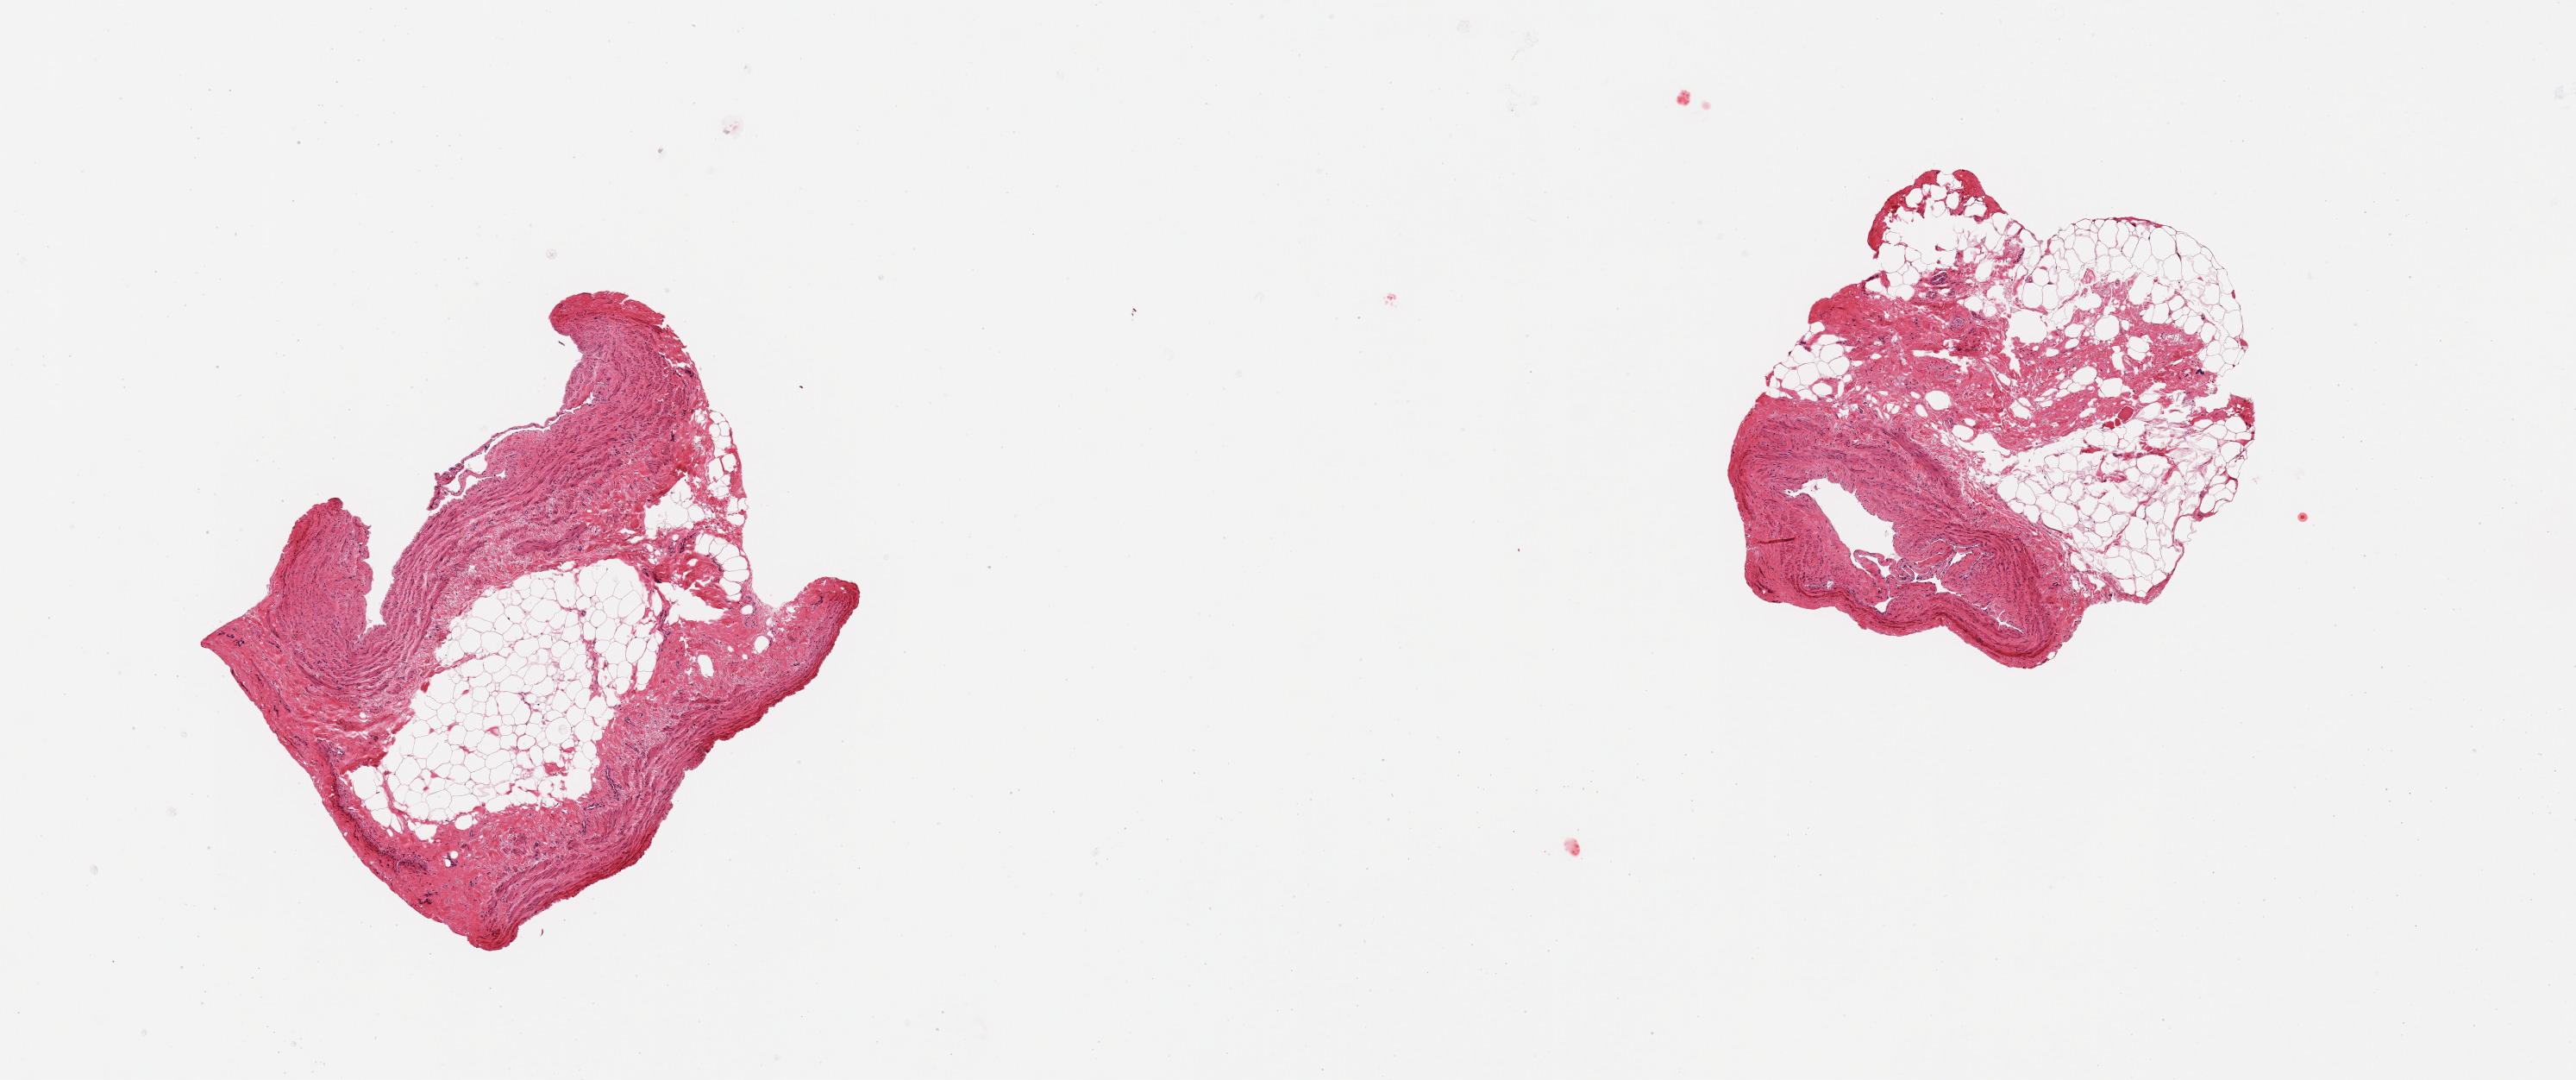
Hematoxylin and eosin (H&E) whole-slide image, a low-resolution overview of the entire scanned area, about 11.8 x 5.0 mm. PAXgene-fixed, paraffin-embedded tissue. Sampled site (target tissue): tibial artery. Tissue donor sample. Donor sex: male.
• reviewer comment on this tissue sample: 2 pieces, mainly fat/fibrous tissue, target artery is <20% specimen